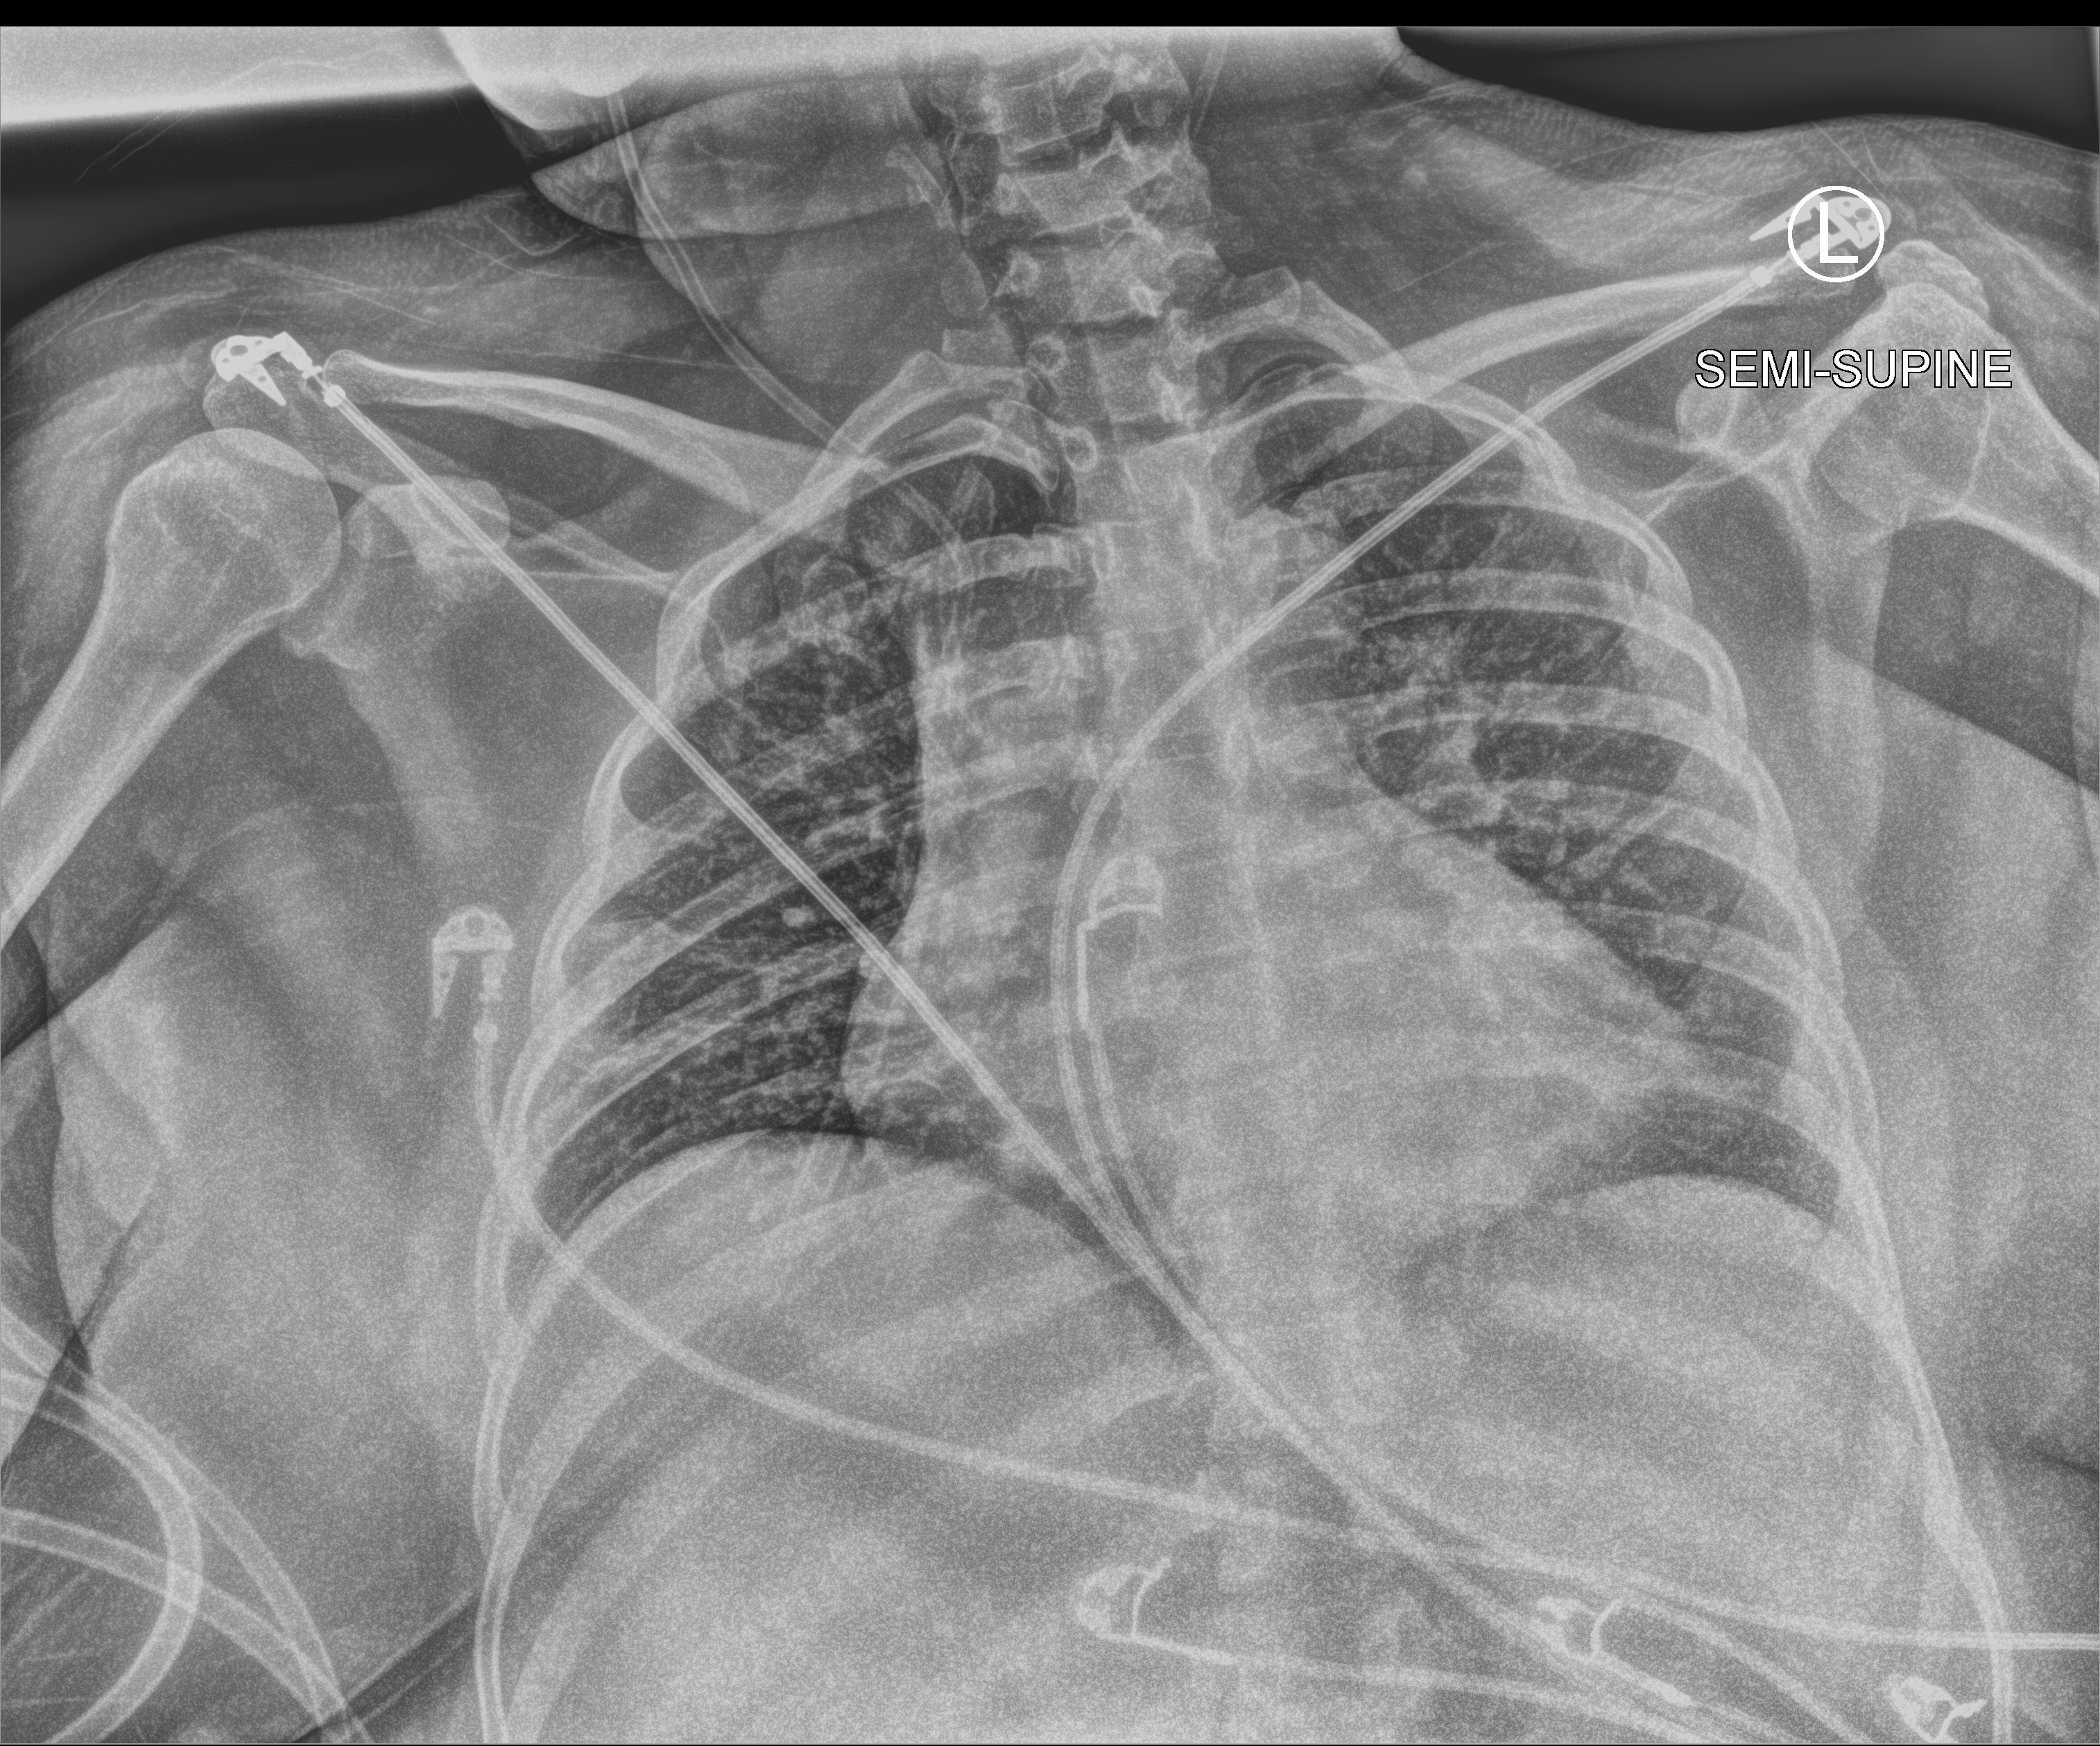
Chest X-ray (portable), anteroposterior (AP) projection. Female patient hospitalised with COVID-19, age 18–59 years.
Admission-level facts for this patient (not findings on this image; timing relative to this image not recorded):
- diabetes (admission record): no
- admitted to intensive care during this hospital stay: no
- mechanically ventilated during this hospital stay: no